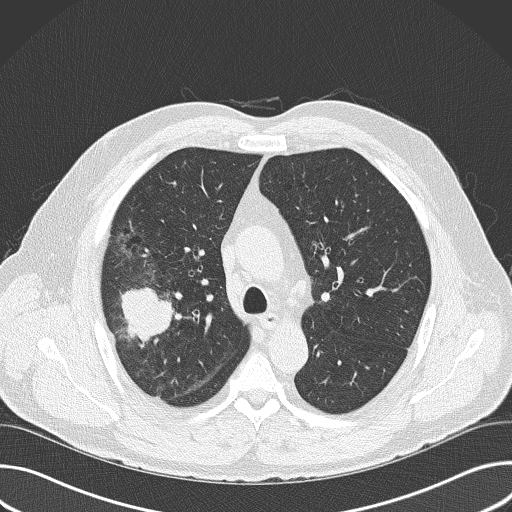
Axial slice from a low-dose chest CT screening exam; baseline screening round; lung window (W 1500 / L -600 HU); 2 mm slice thickness; lung (sharp) reconstruction kernel (B50f); 120 kVp; slice 111 of 157 in the series; 512 × 512 image matrix, field of view 380 × 380 mm. Male, age 56 years at enrolment. Current smoker at enrolment.
Lesion marked by an expert reader, box from (x=83, y=267) to (x=189, y=377) px. Reader record for this screening exam (exam-level; its link to the box is not recorded): non-calcified nodule or mass ≥4 mm, right upper lobe, 6 × 5 mm, spiculated (stellate) margins, soft tissue attenuation. Official screen result: positive, change unspecified: nodule(s) >= 4 mm or enlarging nodule(s), mass(es), or other non-specific abnormalities suspicious for lung cancer. Lung cancer was diagnosed 16 days after this screen: adenocarcinoma, NOS, right upper lobe, poorly differentiated (G3), stage IIB (AJCC 6th edition), 60 mm at pathology.